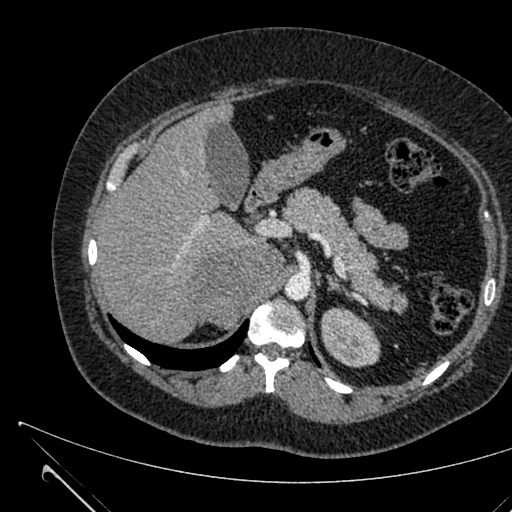
Contrast-enhanced abdominal CT, one axial slice. Slice 444 of 731 in the series (ordered by position). 120 kVp. Intravenous contrast given. Soft-tissue window (W 400 / L 40 HU). 1 mm slice thickness. 512 × 512 image matrix, field of view 376 × 376 mm. Female patient, age 36 years. Case-level facts recorded for this patient, not image findings: diagnosis: adrenocortical carcinoma; tumour side: right adrenal; tumour size at pathology: 10 cm; Ki-67 index: 20 %; stage (as recorded): 4.
Outlined on this slice (semi-automatic segmentation, software-assisted and operator-edited):
- mass: bounding box (x1, y1, x2, y2) in pixels: (195, 244, 280, 325)